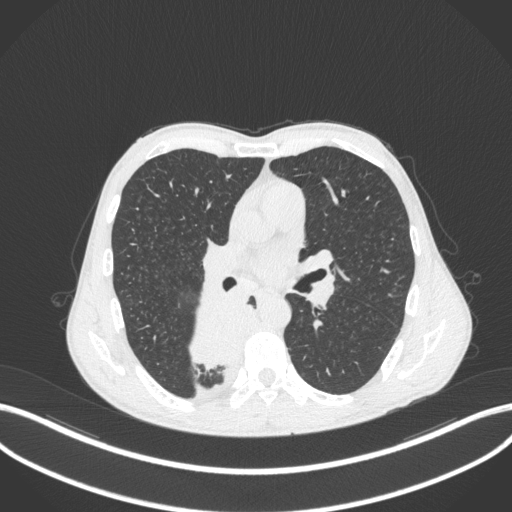
Chest CT, one axial slice; lung window (W 1500 / L -600 HU); 1 mm slice thickness; 512 × 512 image matrix. Male patient, age 58 years. Case-level facts recorded for this patient, not image findings: clinical TNM (as recorded): T3 N1 M1.
Structures marked on this image (bounding box drawn by a radiologist):
- lung tumour (recorded histology: squamous cell carcinoma): bounding box [x1, y1, x2, y2] px = [190, 286, 250, 380]